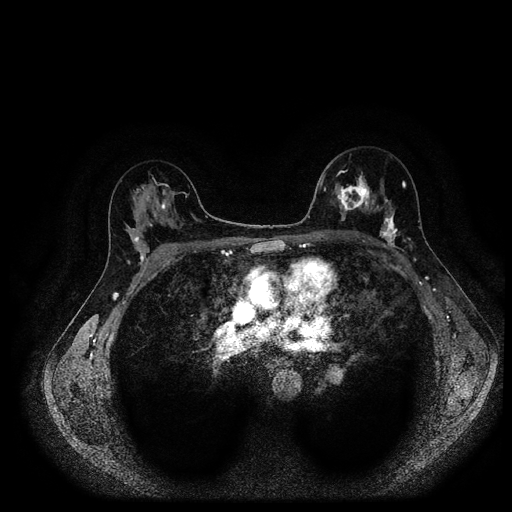
Breast MRI (dynamic contrast-enhanced, multi-phase), one axial slice. Slice 62 of 116 in the series (ordered by position). Dynamic contrast-enhanced series, time point 2 of 5 at this slice position (early post-contrast). 1.5 T. TE 2.7 ms, TR 5.4 ms. 512 × 512 image matrix, field of view 340 × 340 mm. Patient: female, 40 years.
Annotated regions visible in this slice (semi-automatically segmented with operator editing):
- breast lesion (labelled 'tumour' in the annotation; benign lesions carry a separate 'benign' label): box from (x=329, y=172) to (x=373, y=220) px